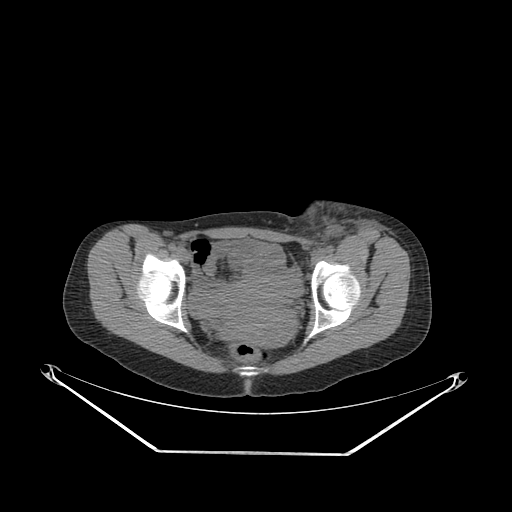
CT of an extremity soft-tissue mass (from a PET/CT study), one axial slice; position 75 of 267 along the scan axis; reconstruction kernel SOFT; 140 kVp; soft-tissue window (W 400 / L 40 HU); 3.75 mm slice thickness; 512 × 512 image matrix, field of view 500 × 500 mm. Female patient. From the clinical record (not read from this slice): histological type: leiomyosarcoma; grade: high; site of the primary tumour: groin.
Annotated regions visible in this slice (expert contour drawn on MRI and transferred to this co-registered scan by the dataset authors):
- gross tumour volume including surrounding oedema: bounding box (x1, y1, x2, y2) in pixels: (285, 203, 389, 252)
- gross tumour volume (mass): (290, 205, 343, 252)